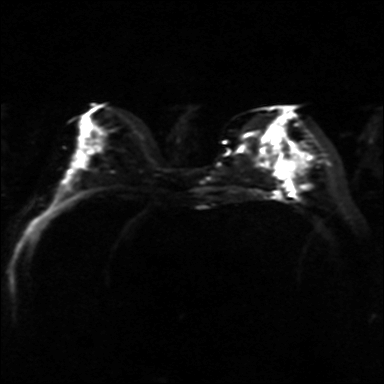
Breast MRI, one axial slice. Slice 16 of 36 in the series (ordered by position). Diffusion-weighted series; image 2 of 4 stored at this slice position (different b-values; order by instance number). 3 T. 4 mm slice thickness. 384 × 384 image matrix, field of view 320 × 320 mm. Female patient.
Outlined on this slice (outlined manually by an expert reader):
- tumour on diffusion-weighted imaging: box from (x=278, y=163) to (x=289, y=177) px